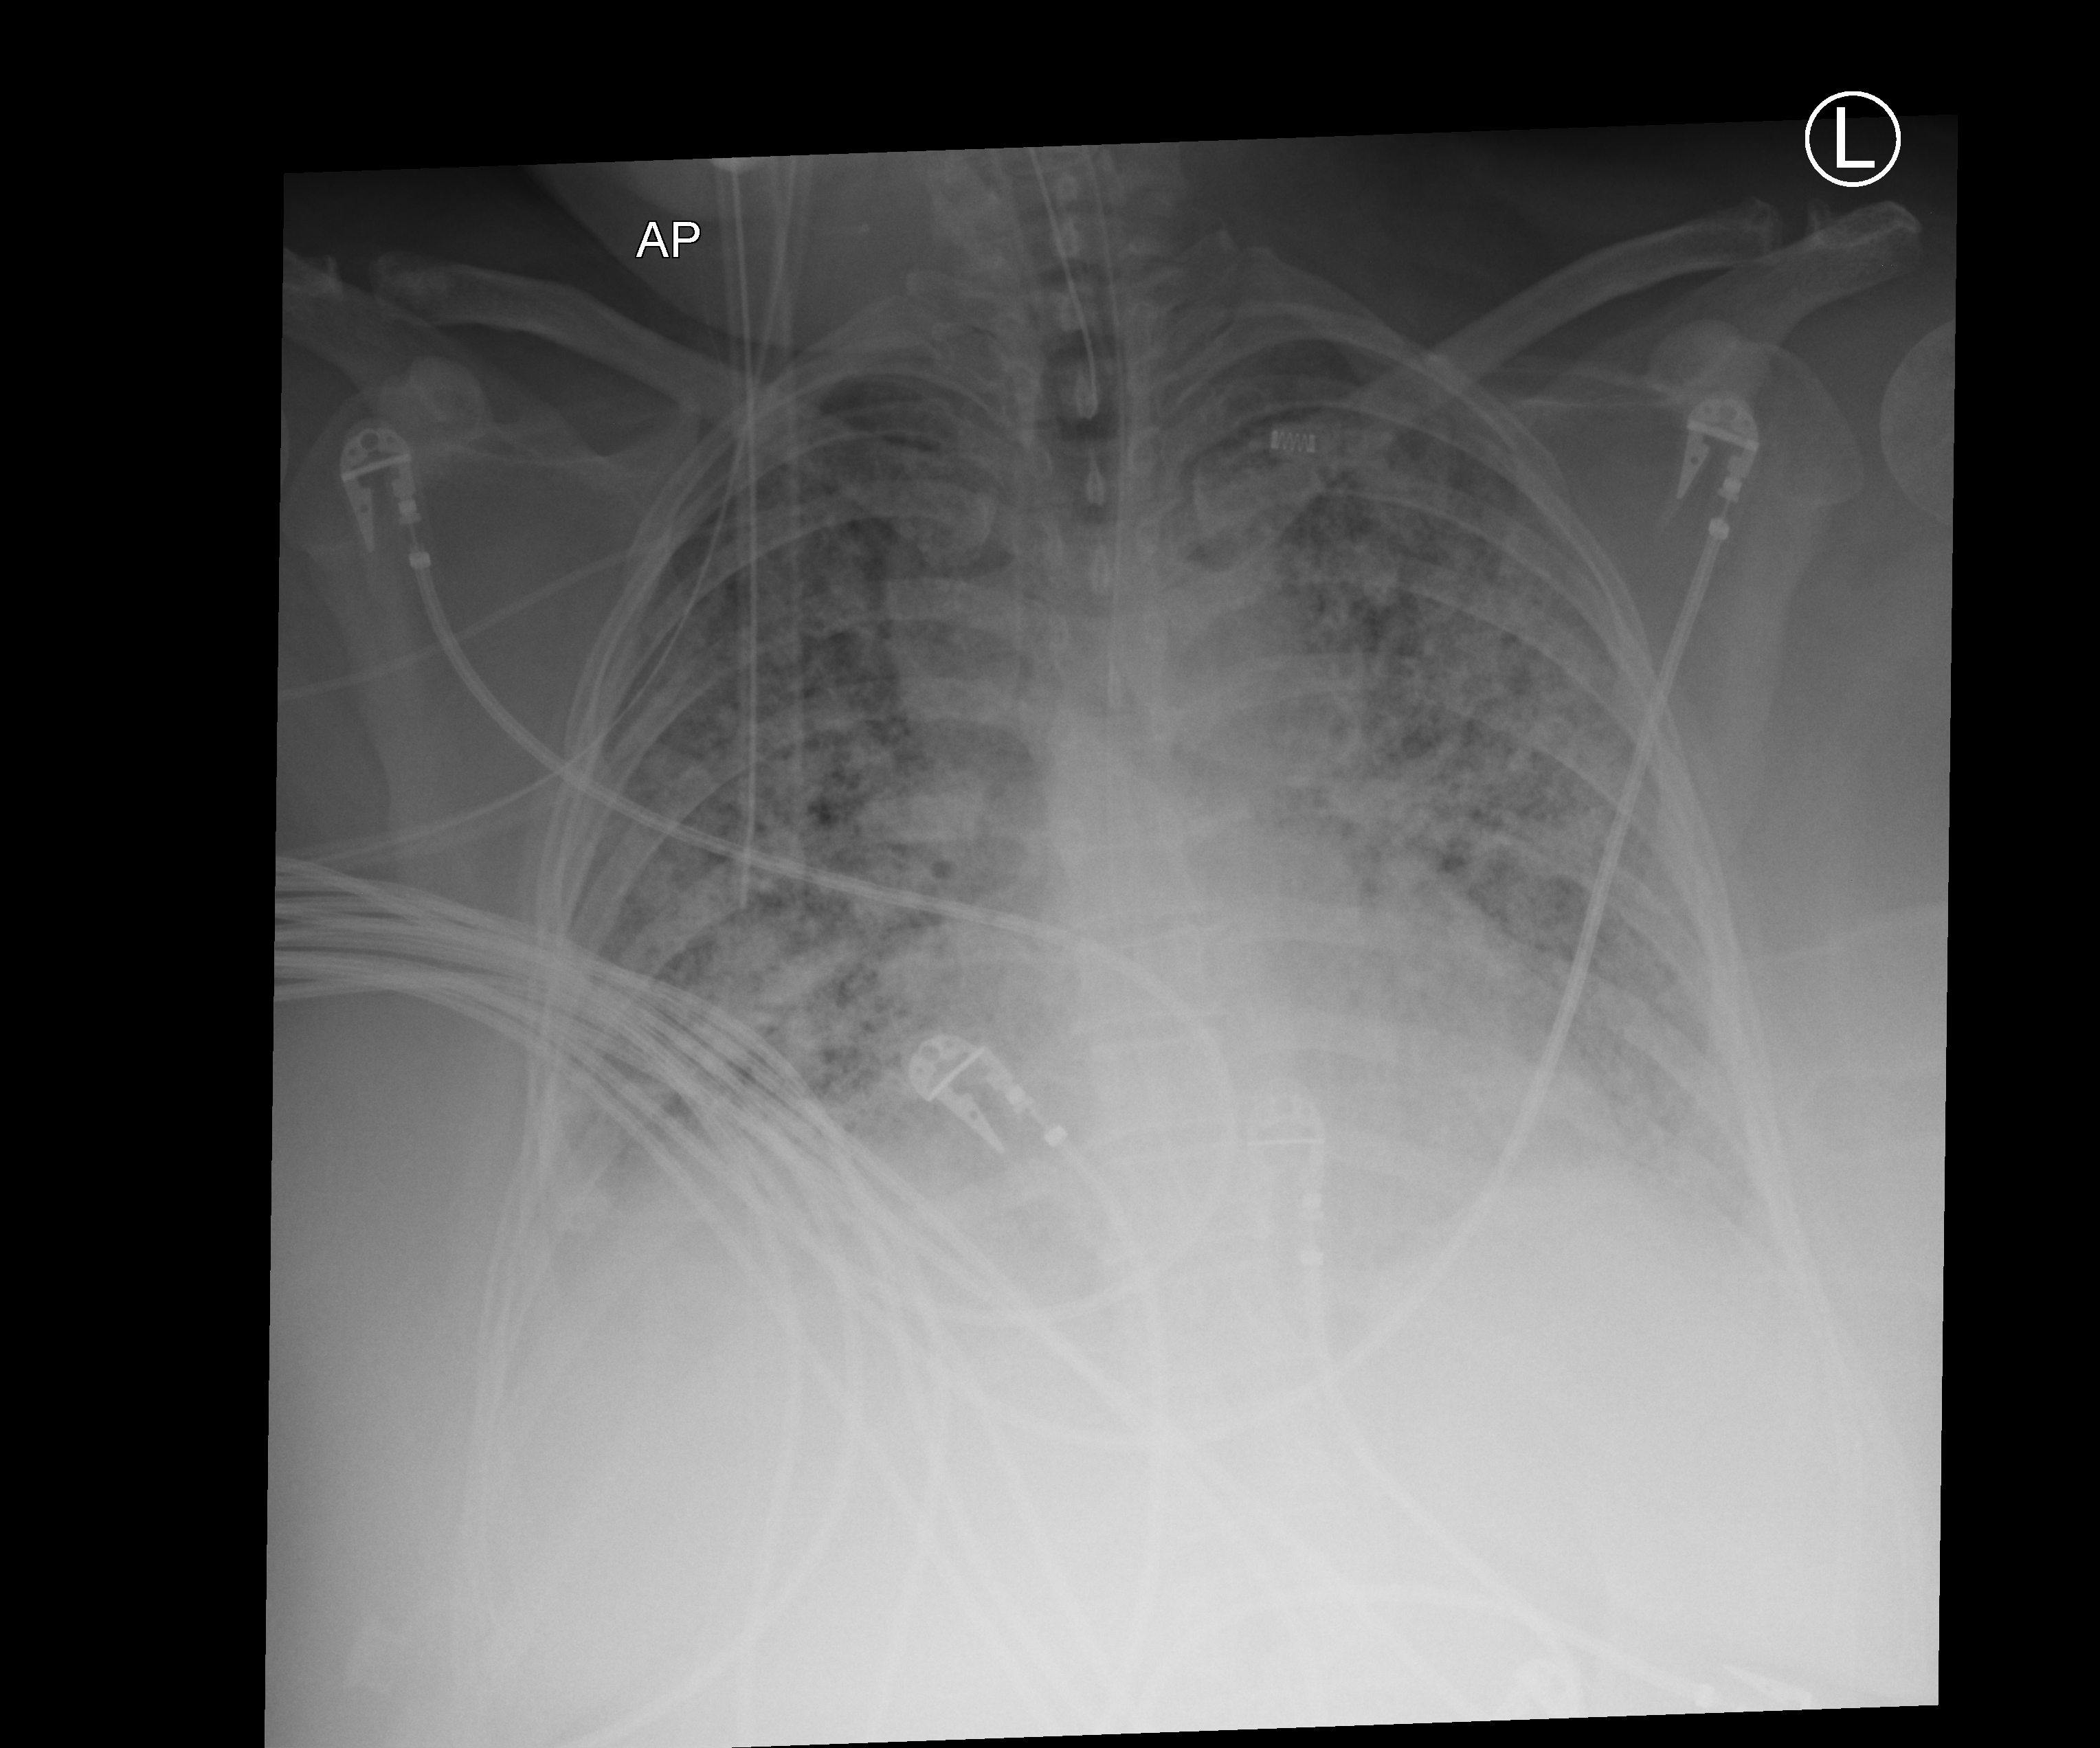
Chest X-ray (portable); anteroposterior (AP) projection. Female patient hospitalised with COVID-19, age 18–59 years.
Admission-level facts for this patient (not findings on this image; timing relative to this image not recorded): length of hospital stay: 95 days.